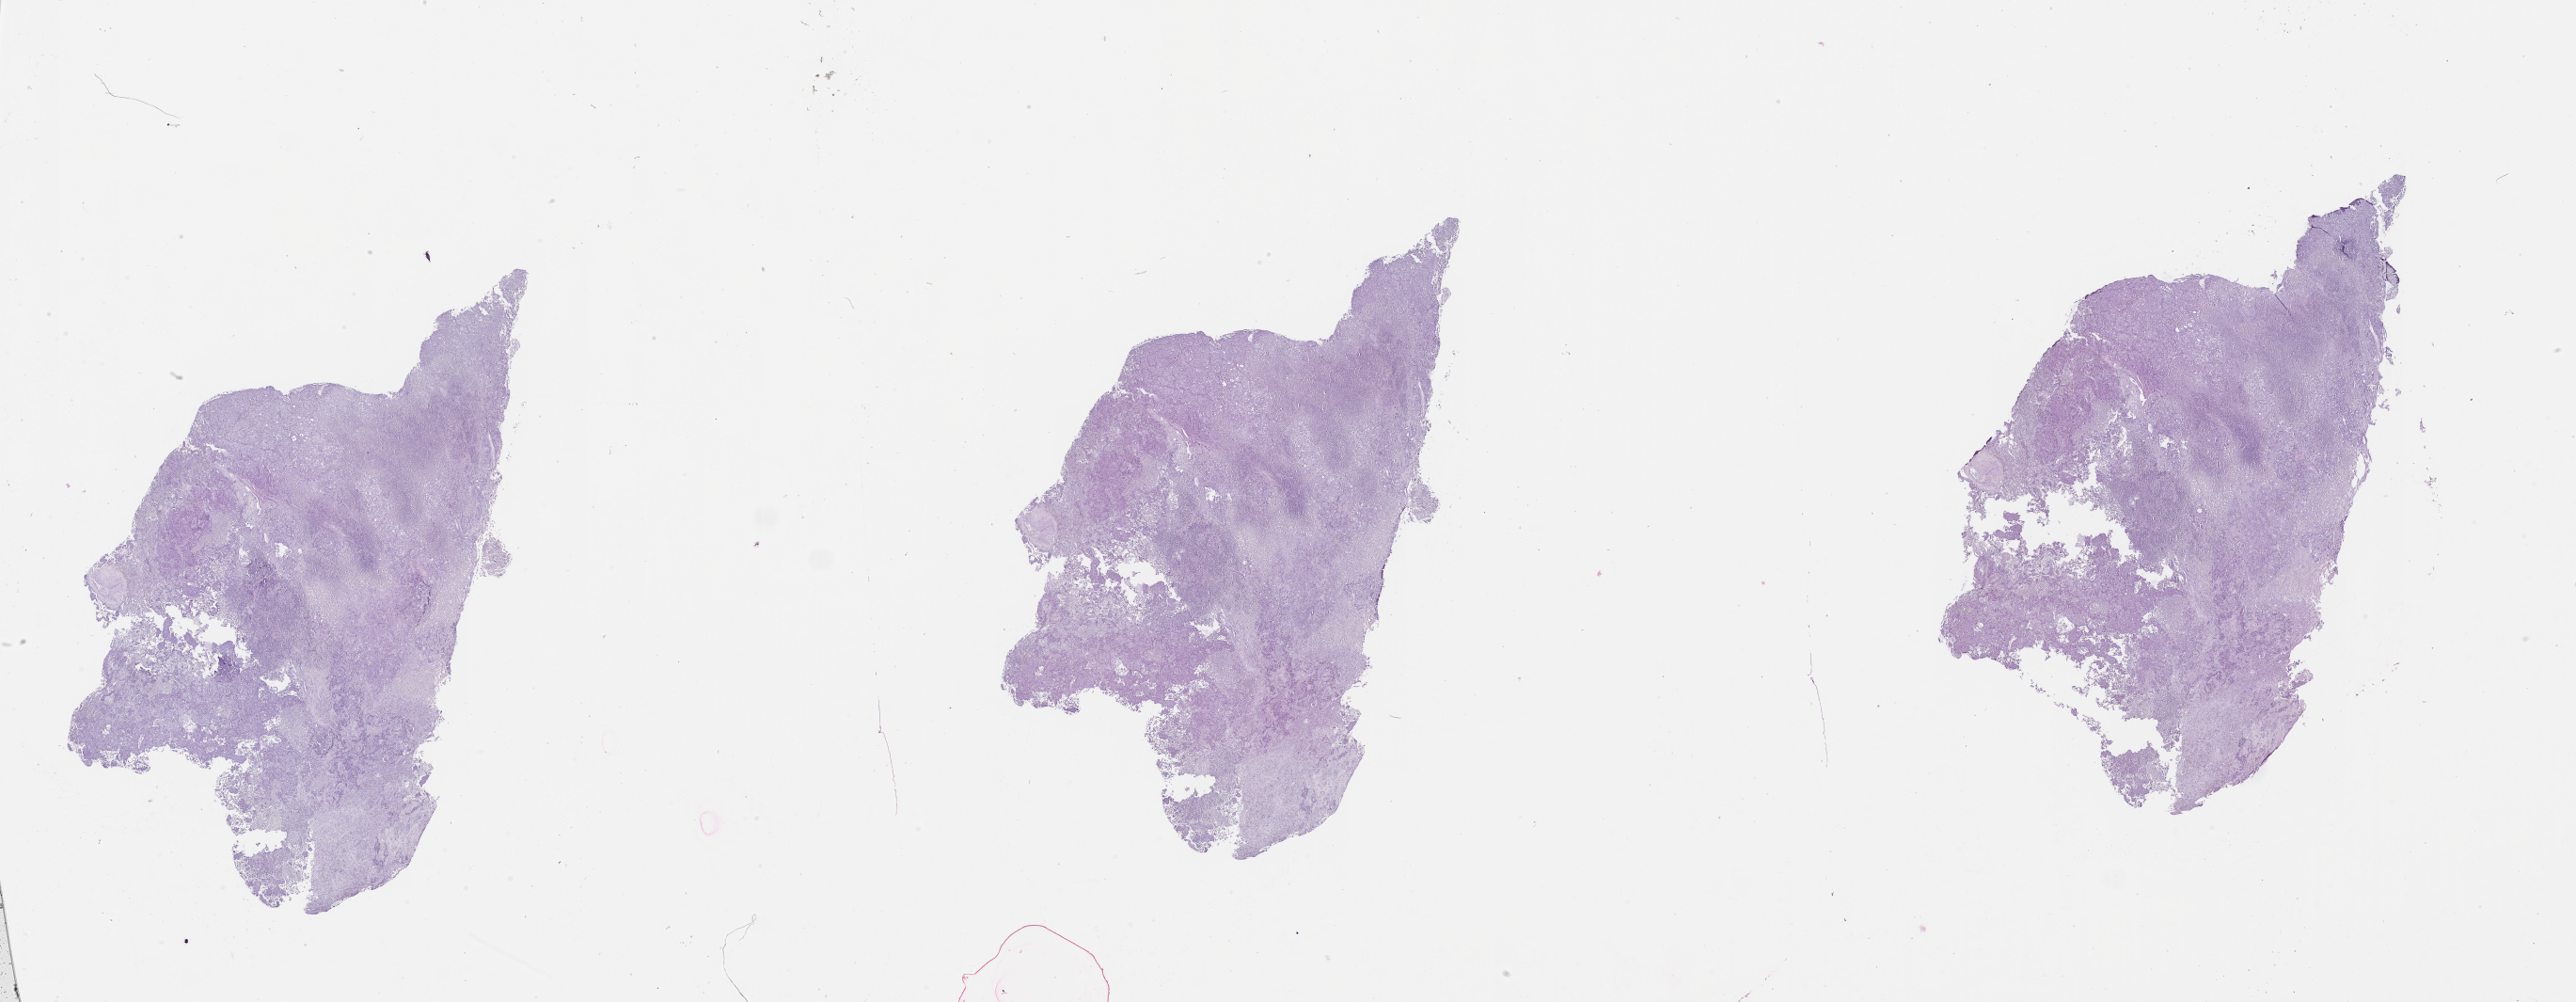
Digitized H&E tissue section (whole slide), low-resolution overview of the scanned area, about 44.1 x 17.1 mm (acquisition: 20x scan); lung, tissue type not recorded.
* patient diagnosis (cohort enrolment): lung adenocarcinoma (lung)